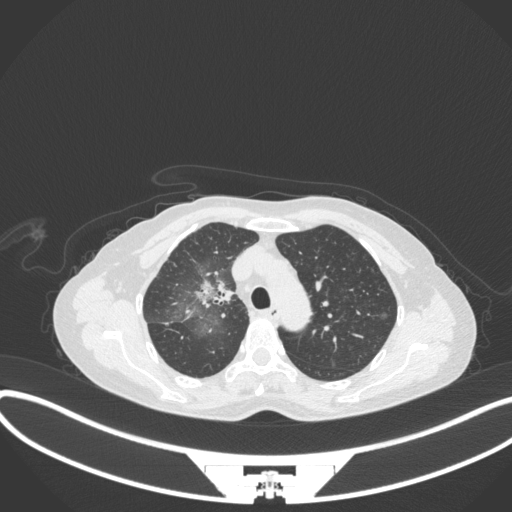
Chest CT, one axial slice; slice 231 of 311 in the series (ordered by position); reconstruction kernel B31f; 120 kVp; lung window (W 1500 / L -600 HU); 1 mm slice thickness; 512 × 512 image matrix, field of view 400 × 400 mm. Female patient, age 59 years. Case-level facts recorded for this patient, not image findings: clinical TNM (as recorded): T3 N0 M0; histopathological grade: G1.
Outlined on this slice (rectangle marked by the reading radiologist):
- lung tumour (recorded histology: adenocarcinoma): bounding box [x1, y1, x2, y2] px = [190, 272, 234, 312]